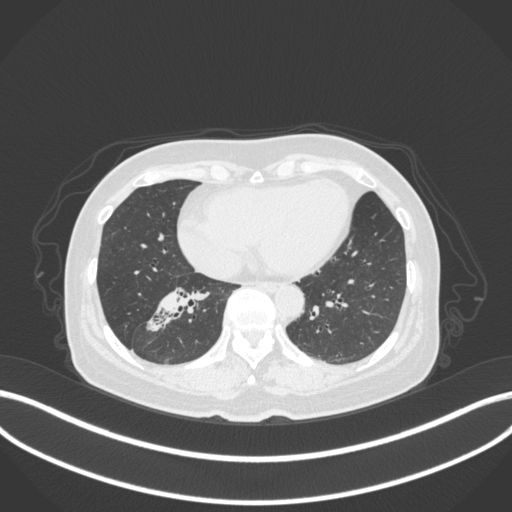
Chest CT, one axial slice; position 138 of 429 along the scan axis; 120 kVp; lung window (W 1500 / L -600 HU); 512 × 512 image matrix. Patient: female, 67 years. From the clinical record (not read from this slice): clinical TNM (as recorded): T1c N1 M0.
Outlined on this slice (rectangle marked by the reading radiologist):
- lung tumour (recorded histology: adenocarcinoma): bounding box [x1, y1, x2, y2] px = [140, 278, 215, 338]